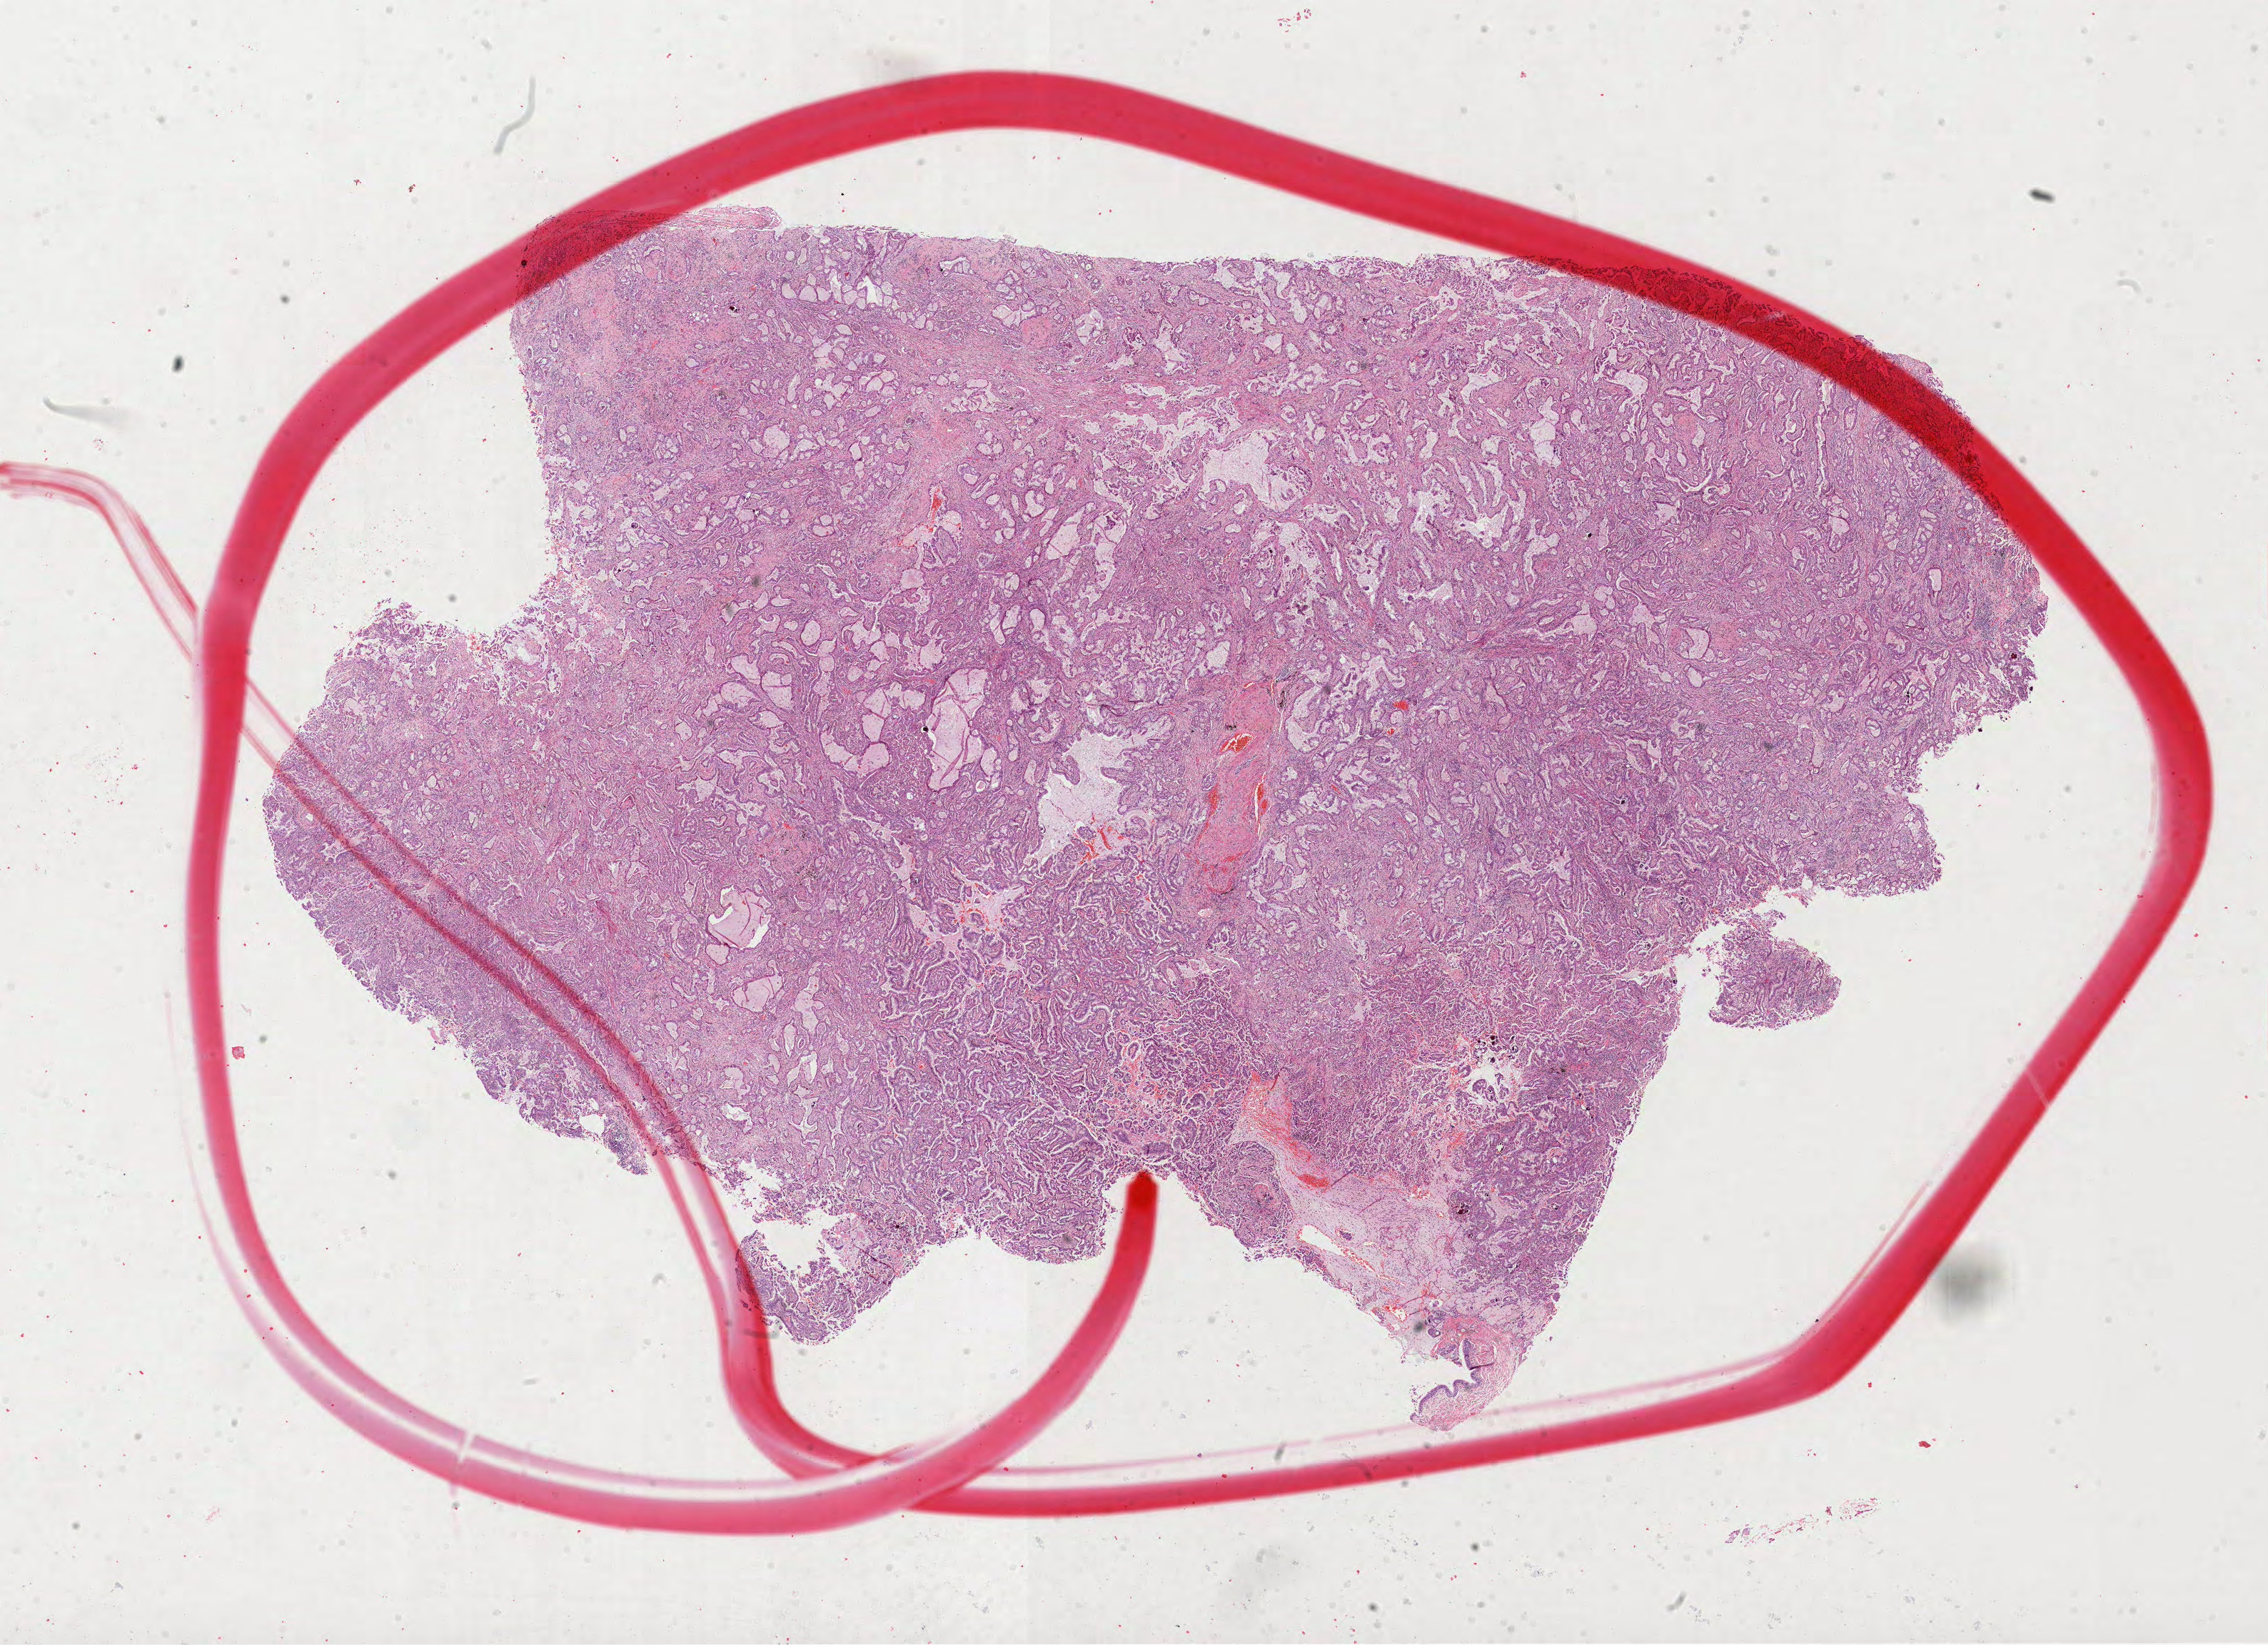
Digitized H&E tissue section (whole slide), a low-resolution overview of the entire scanned area, about 25.6 x 18.6 mm (slide scanned at 40x), formalin-fixed paraffin-embedded (FFPE) diagnostic section, primary tumour sample from the lung. Patient: female, age at initial diagnosis 63 years.
Diagnosis: Mucinous adenocarcinoma (lower lobe, lung). AJCC pathologic stage: IIB (7th edition). Laterality: left.